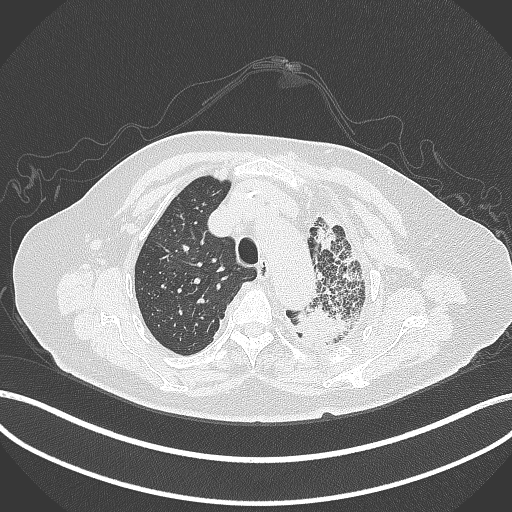
Chest CT, one axial slice. Position 308 of 399 along the scan axis. Reconstruction kernel B70f. 120 kVp. Lung window (W 1500 / L -600 HU). 512 × 512 image matrix. Female patient, age 75 years. Case-level facts recorded for this patient, not image findings: clinical TNM (as recorded): T3 N3 M1.
Annotated regions visible in this slice (rectangle marked by the reading radiologist):
- lung tumour (recorded histology: adenocarcinoma): bounding box [x1, y1, x2, y2] px = [292, 293, 360, 348]